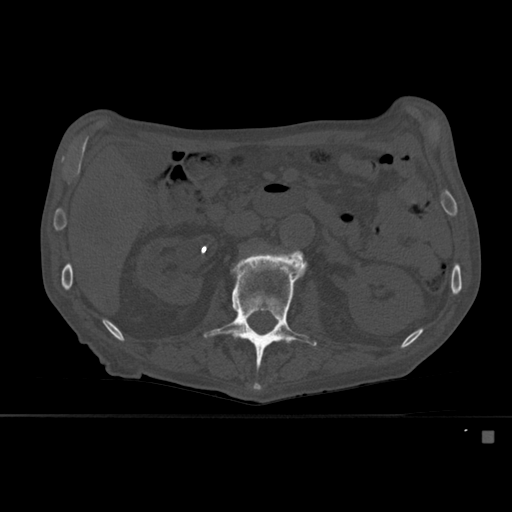
CT including the spine, one axial slice; slice 235 of 527 in the series (ordered by position); bone window (W 1800 / L 400 HU); 1.5 mm slice thickness; 512 × 512 image matrix, field of view 373 × 373 mm. Patient: male, 78 years. Case-level facts recorded for this patient, not image findings: primary cancer: prostate.
Structures marked on this image (semi-automatic segmentation, software-assisted and operator-edited):
- L2 vertebra: bounding box <203,250,317,390> (left, top, right, bottom; pixels)